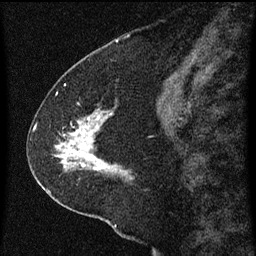
Breast MRI (dynamic contrast-enhanced), one sagittal slice; slice 28 of 60 in the series (ordered by position); dynamic contrast-enhanced series, image 2 of 3 at this slice position (ordered by acquisition); 1.5 T; TE 4.2 ms, TR 8 ms; 256 × 256 image matrix, field of view 180 × 180 mm. Patient: female, 47 years.
Annotated regions visible in this slice (semi-automatic segmentation, software-assisted and operator-edited):
- analysis volume of interest (the breast-tissue region the enhancement analysis was run in; not a lesion): bounding box <36,96,135,213> (left, top, right, bottom; pixels)
- tumour enhancement mask (voxels above the 70 % enhancement threshold inside the analysis volume of interest): <56,112,113,173>